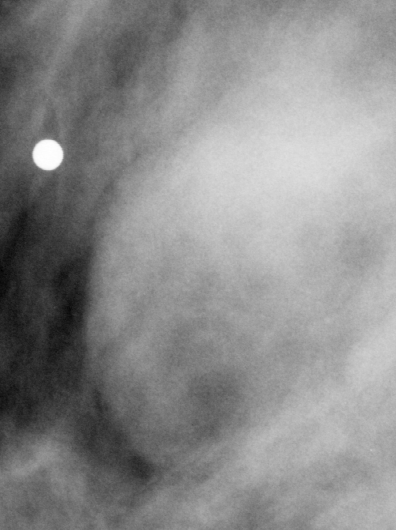
Region of interest cut from a scanned film mammogram (one marked finding), right breast, MLO view.
Finding: mass, shape oval, margins obscured; BI-RADS assessment category 3; subtlety rating 4 on a 1 (subtle) to 5 (obvious) scale; pathology (as recorded): benign.